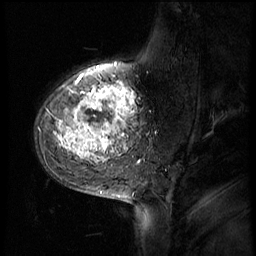
Breast MRI (dynamic contrast-enhanced), one sagittal slice. Position 15 of 56 along the scan axis. 4 images stored at this slice position (order not interpretable as contrast timing). 1.5 T. TE 4.2 ms, TR 8.9 ms. 256 × 256 image matrix, field of view 220 × 220 mm. Patient: female, 51 years. From the clinical record (not read from this slice): setting: breast cancer imaged before/during neoadjuvant chemotherapy; receptor status: triple-negative.
Annotated regions visible in this slice (semi-automatically segmented with operator editing):
- analysis volume of interest (the breast-tissue region the enhancement analysis was run in; not a lesion): box from (x=35, y=70) to (x=150, y=173) px
- tumour enhancement mask (voxels above the 140 % enhancement threshold inside the analysis volume of interest): (x=57, y=76)–(x=137, y=161)